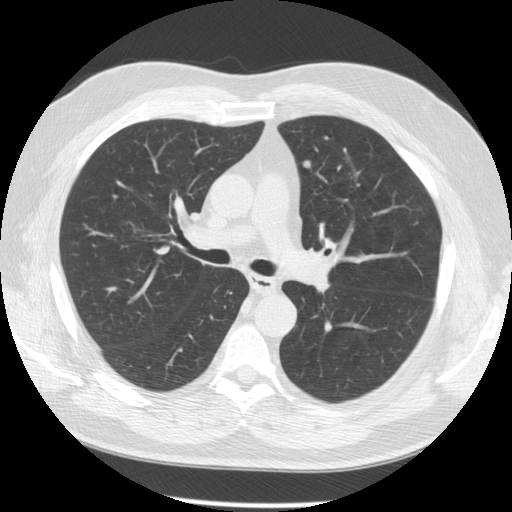
Axial slice from a low-dose chest CT screening exam. Second screening round (one year after baseline). Lung window (W 1500 / L -600 HU). 2.5 mm slice thickness. Standard (soft-tissue) reconstruction kernel (STANDARD). Male participant, aged 64 years at enrolment.
Lesion marked by an expert reader, bounding box (x1, y1, x2, y2) in pixels: (287, 146, 324, 185). The screening reader recorded 2 non-calcified nodules or masses ≥4 mm on this exam (left upper lobe, left lower lobe); which of them this box marks is not recorded. Official screen result: positive, other. Later outcome: lung cancer diagnosed 58 days after this screen — squamous cell carcinoma, NOS, left upper lobe, poorly differentiated (G3), stage IA (AJCC 6th edition), 14 mm at pathology.